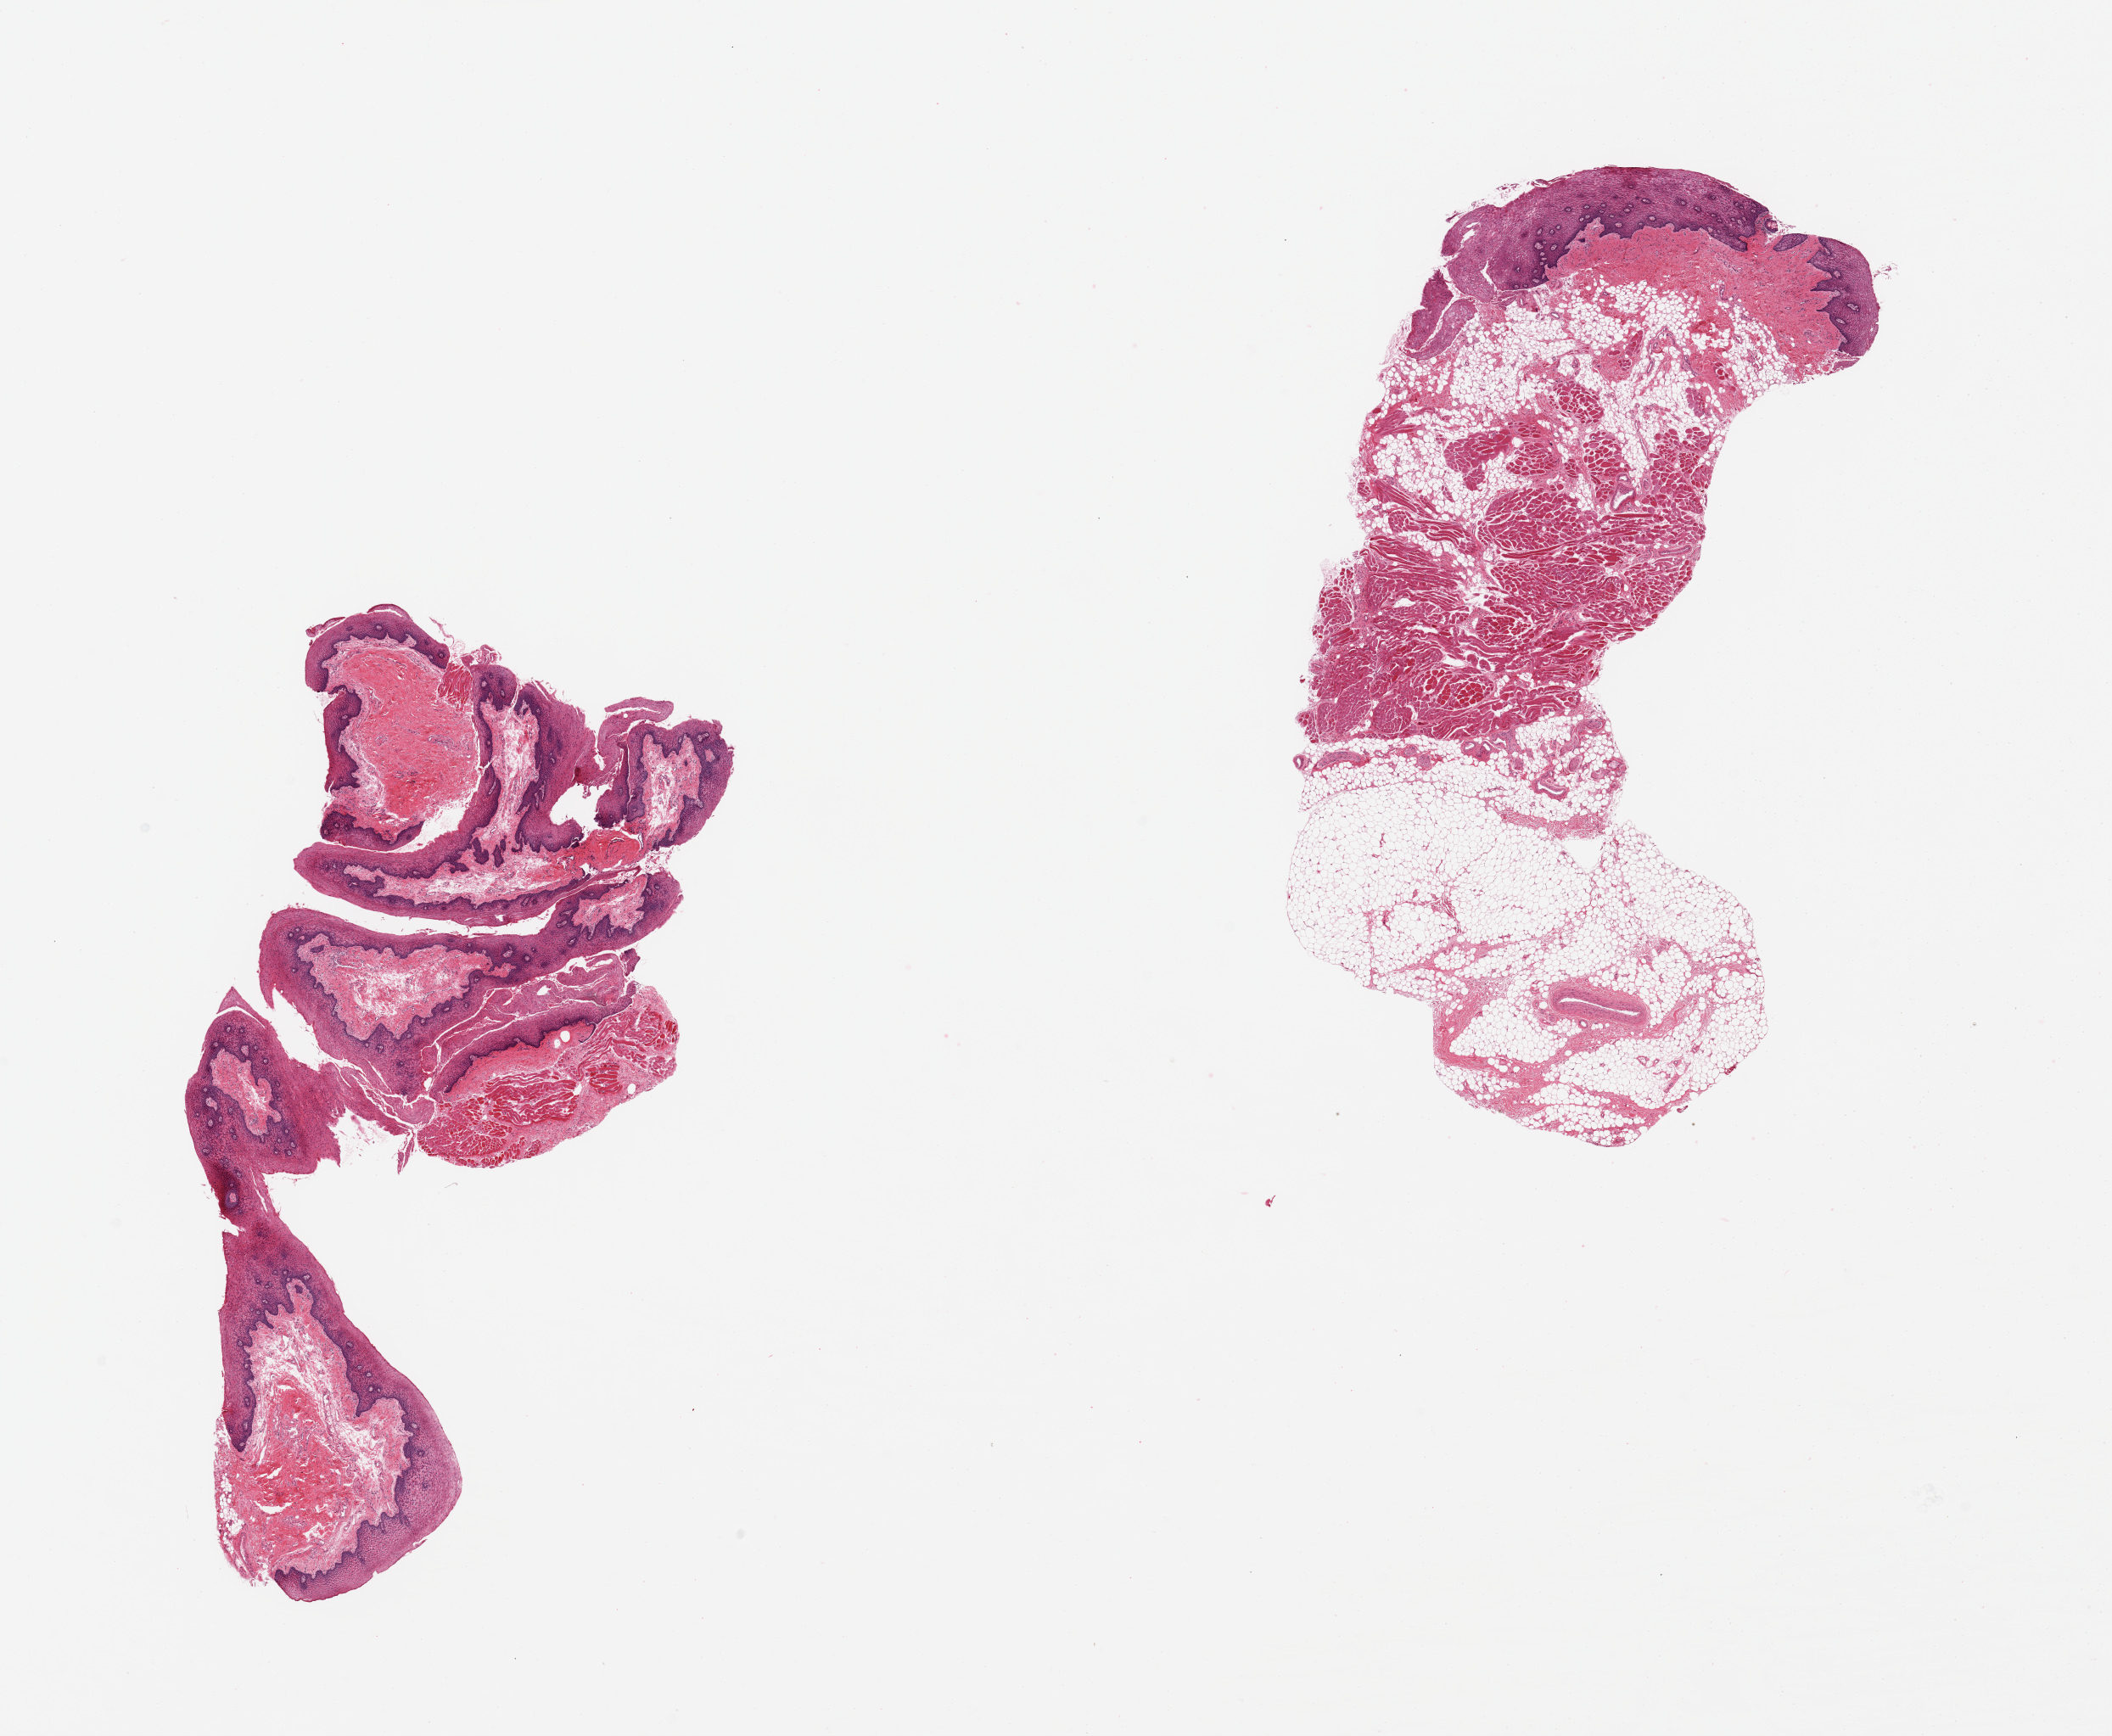
Whole-slide image, haematoxylin and eosin stain — a low-resolution overview of the entire scanned area, about 19.7 x 16.2 mm; PAXgene-fixed paraffin-embedded (PFPE) section; sampled site (target tissue): minor salivary gland; donor tissue sample. Male donor.
Pathologist's review note for this sample: 2 pieces all squamous mucoa/stroma, no glandular tissue.